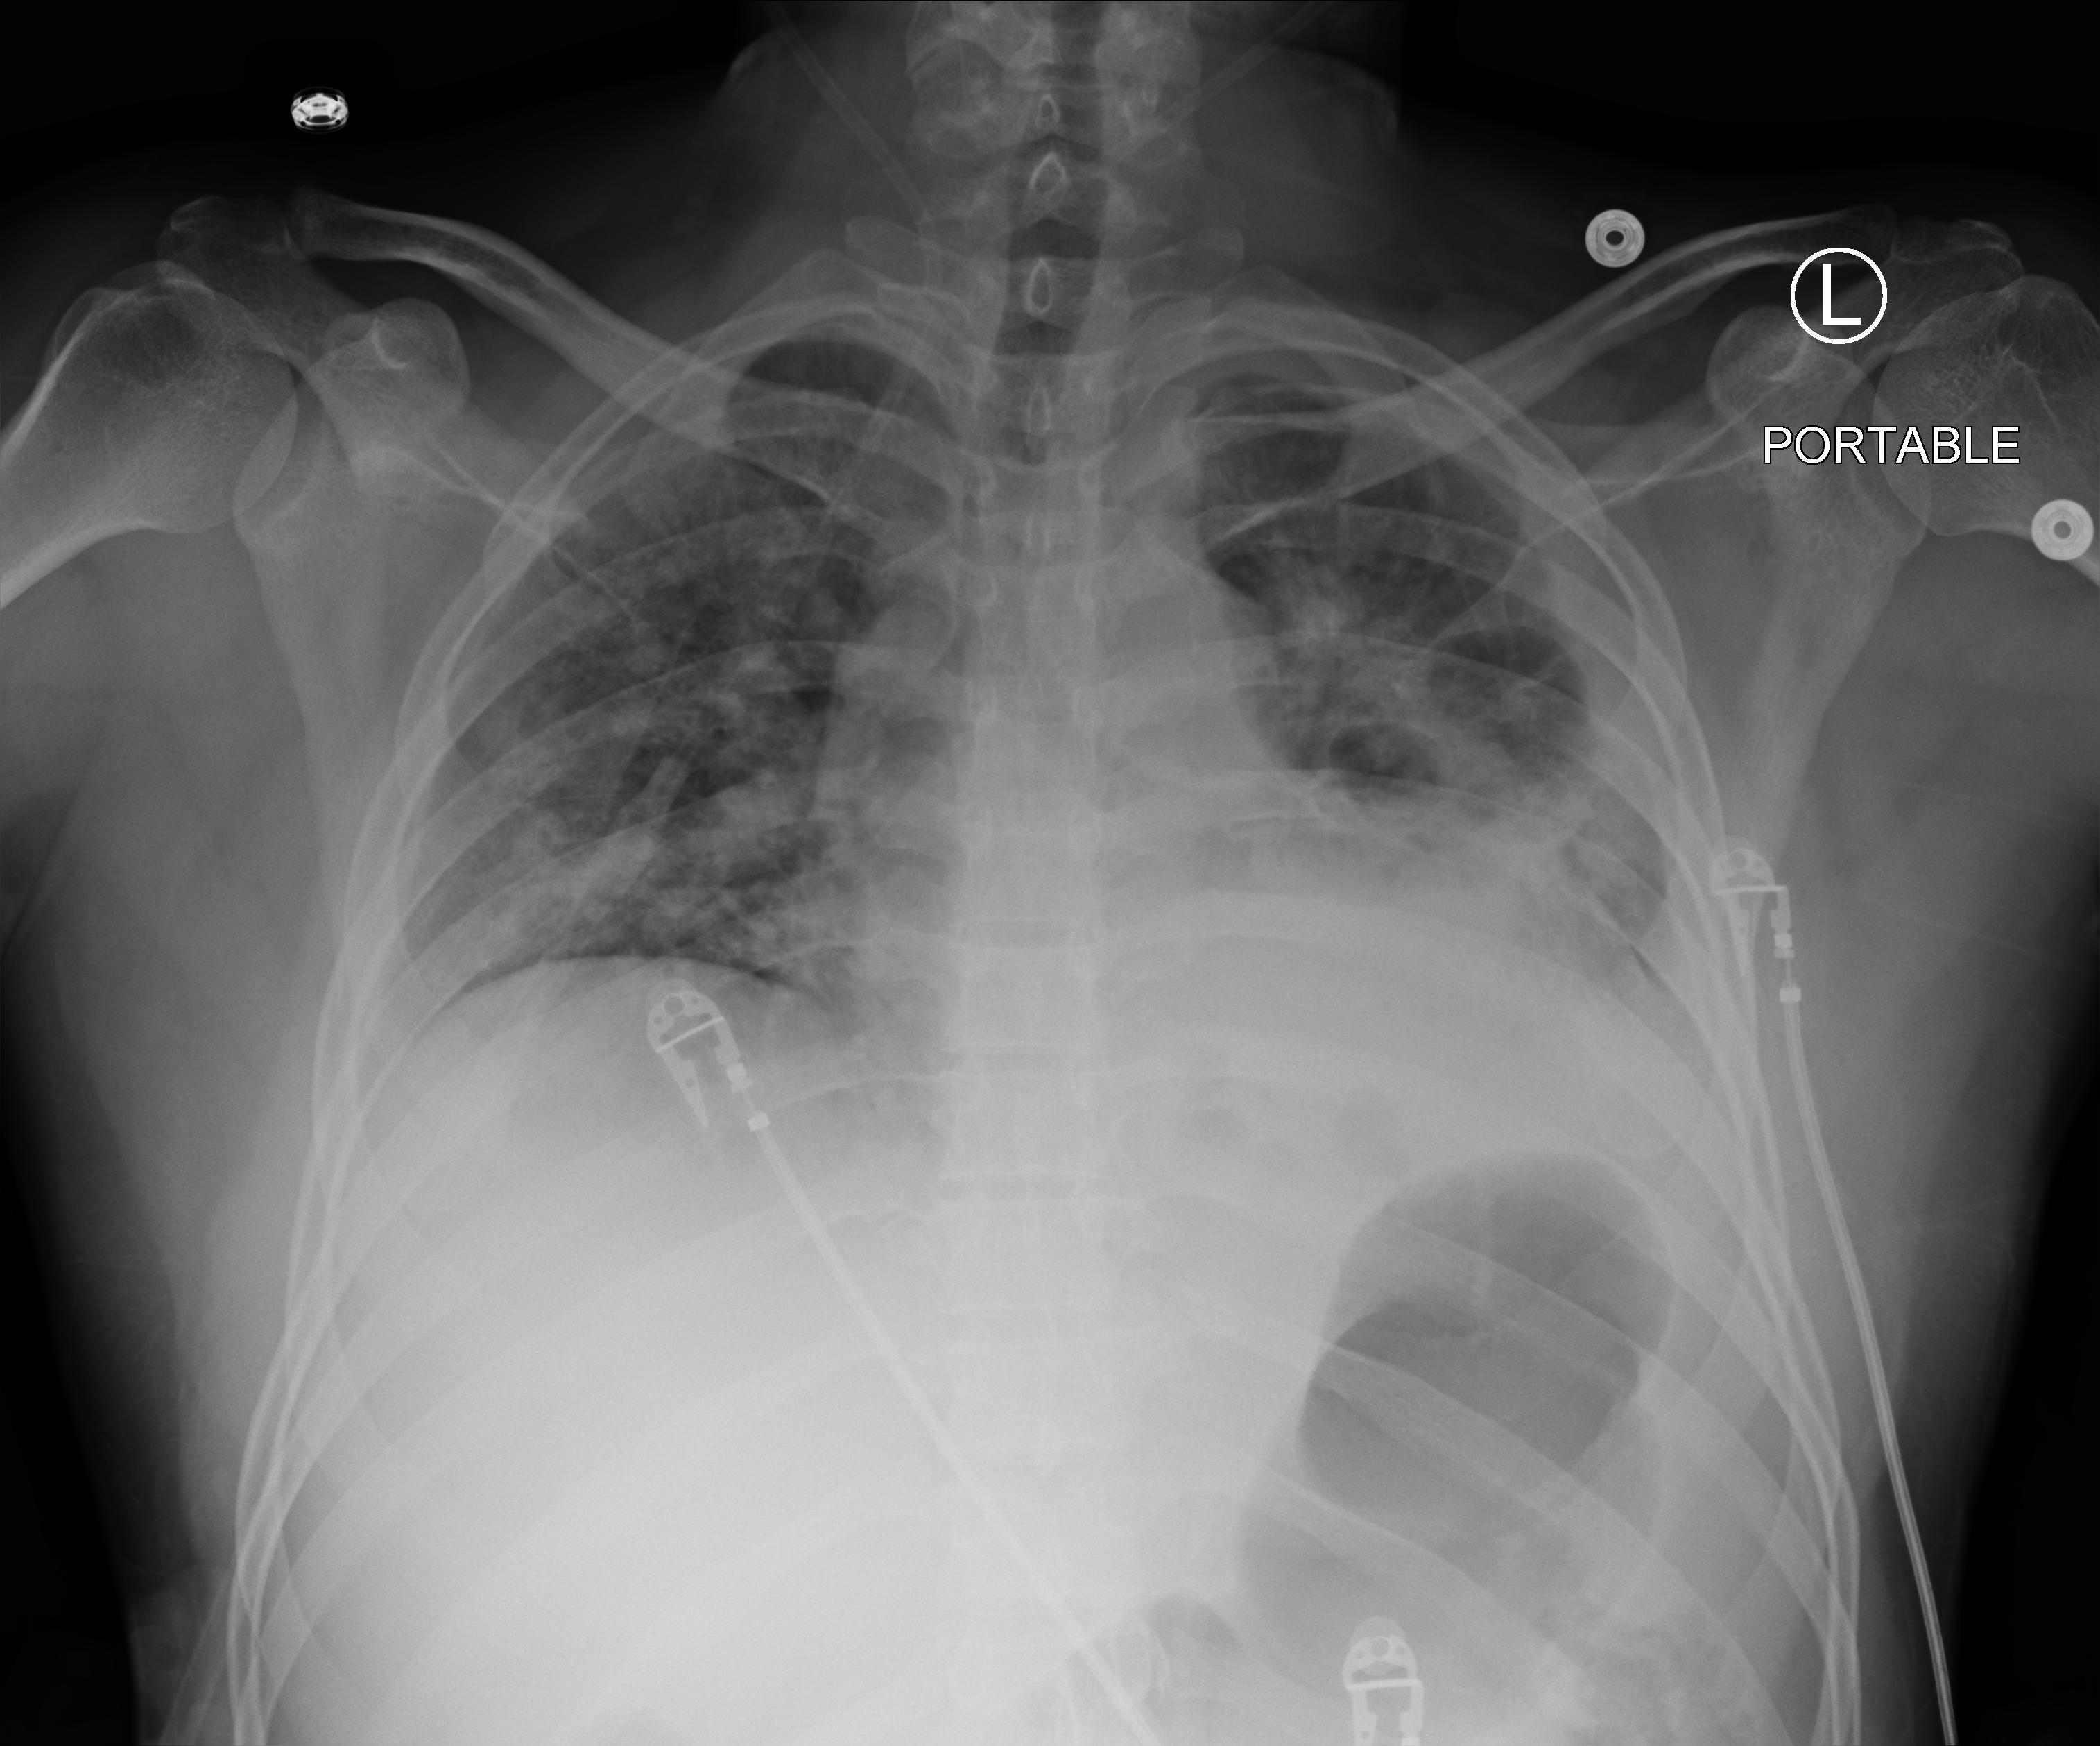
Bedside chest radiograph (computed radiography); anteroposterior (AP) projection. Patient hospitalised with COVID-19; male, aged 18–59 years.
Admission-level facts for this patient (not findings on this image; timing relative to this image not recorded):
- admitted to intensive care during this hospital stay: yes
- smoking status (admission record): never